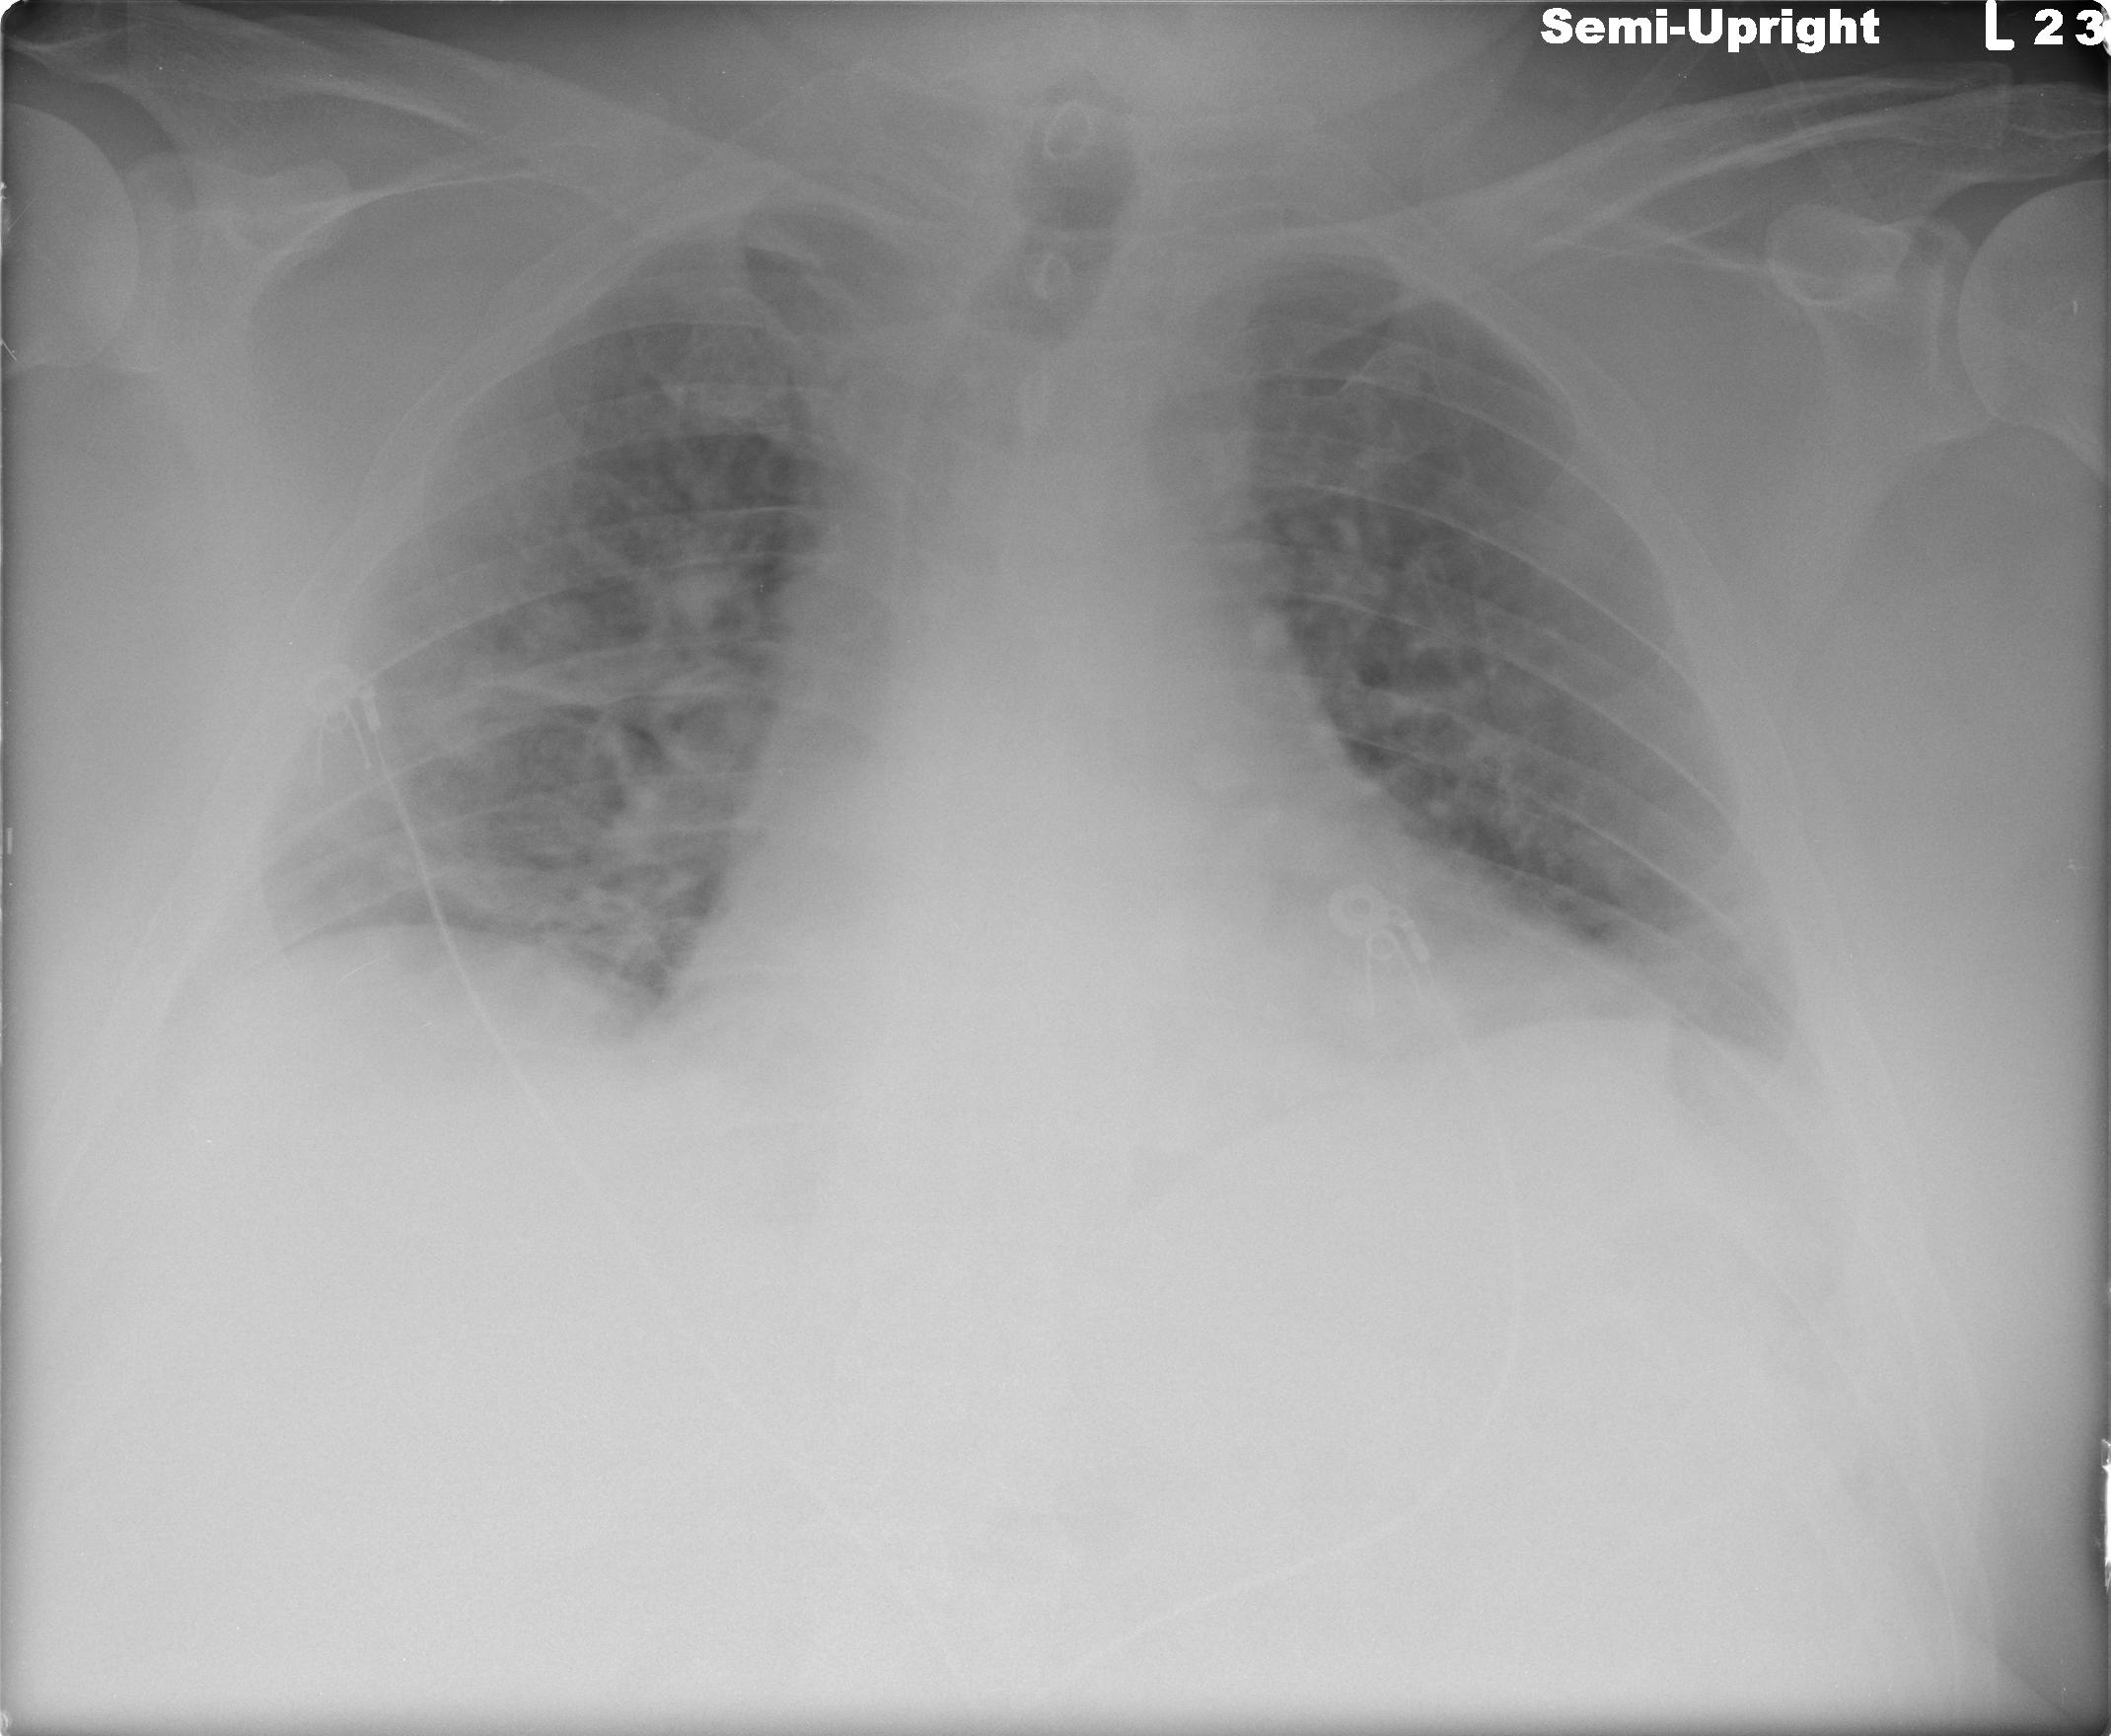
Portable chest radiograph, AP projection. Male patient, age 61 years; imaged 4 days after the COVID-19 diagnosis.
Radiologist's key findings for this exam: ncreased bilateral lower lung and right midlung airspace opacities.